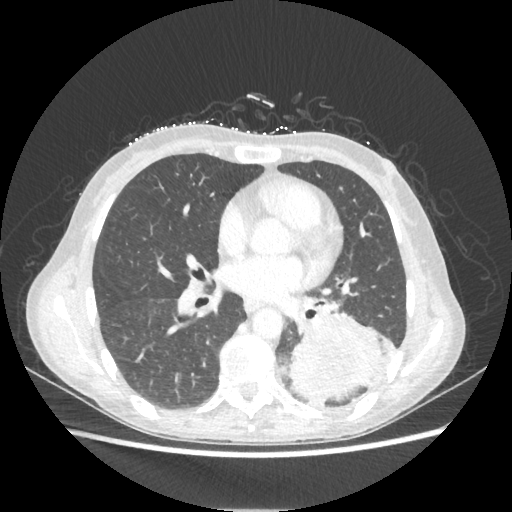
Chest CT, one axial slice. Position 108 of 221 along the scan axis. 80 kVp. Lung window (W 1500 / L -600 HU). 1.25 mm slice thickness. 512 × 512 image matrix, field of view 360 × 360 mm. Female patient, age 53 years. Case-level facts recorded for this patient, not image findings: clinical TNM (as recorded): T3 N0 M0.
Outlined on this slice (rectangle marked by the reading radiologist):
- lung tumour (recorded histology: adenocarcinoma): bounding box (x1, y1, x2, y2) in pixels: (289, 310, 390, 407)